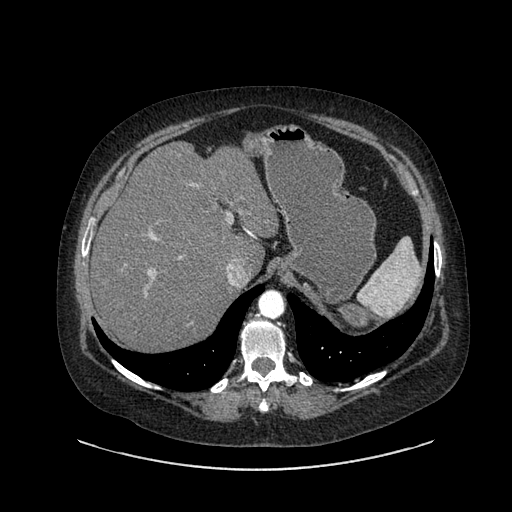
Contrast-enhanced abdominal CT, one axial slice; intravenous contrast given; soft-tissue window (W 400 / L 40 HU); 512 × 512 image matrix. Female patient, age 61 years. Case-level facts recorded for this patient, not image findings: diagnosis: adrenocortical carcinoma; tumour side: left adrenal; tumour size at pathology: 13 cm; Ki-67 index: 79 %; stage (as recorded): 2.
Annotated regions visible in this slice (semi-automatically segmented with operator editing):
- mass: bounding box [x1, y1, x2, y2] px = [337, 302, 370, 334]